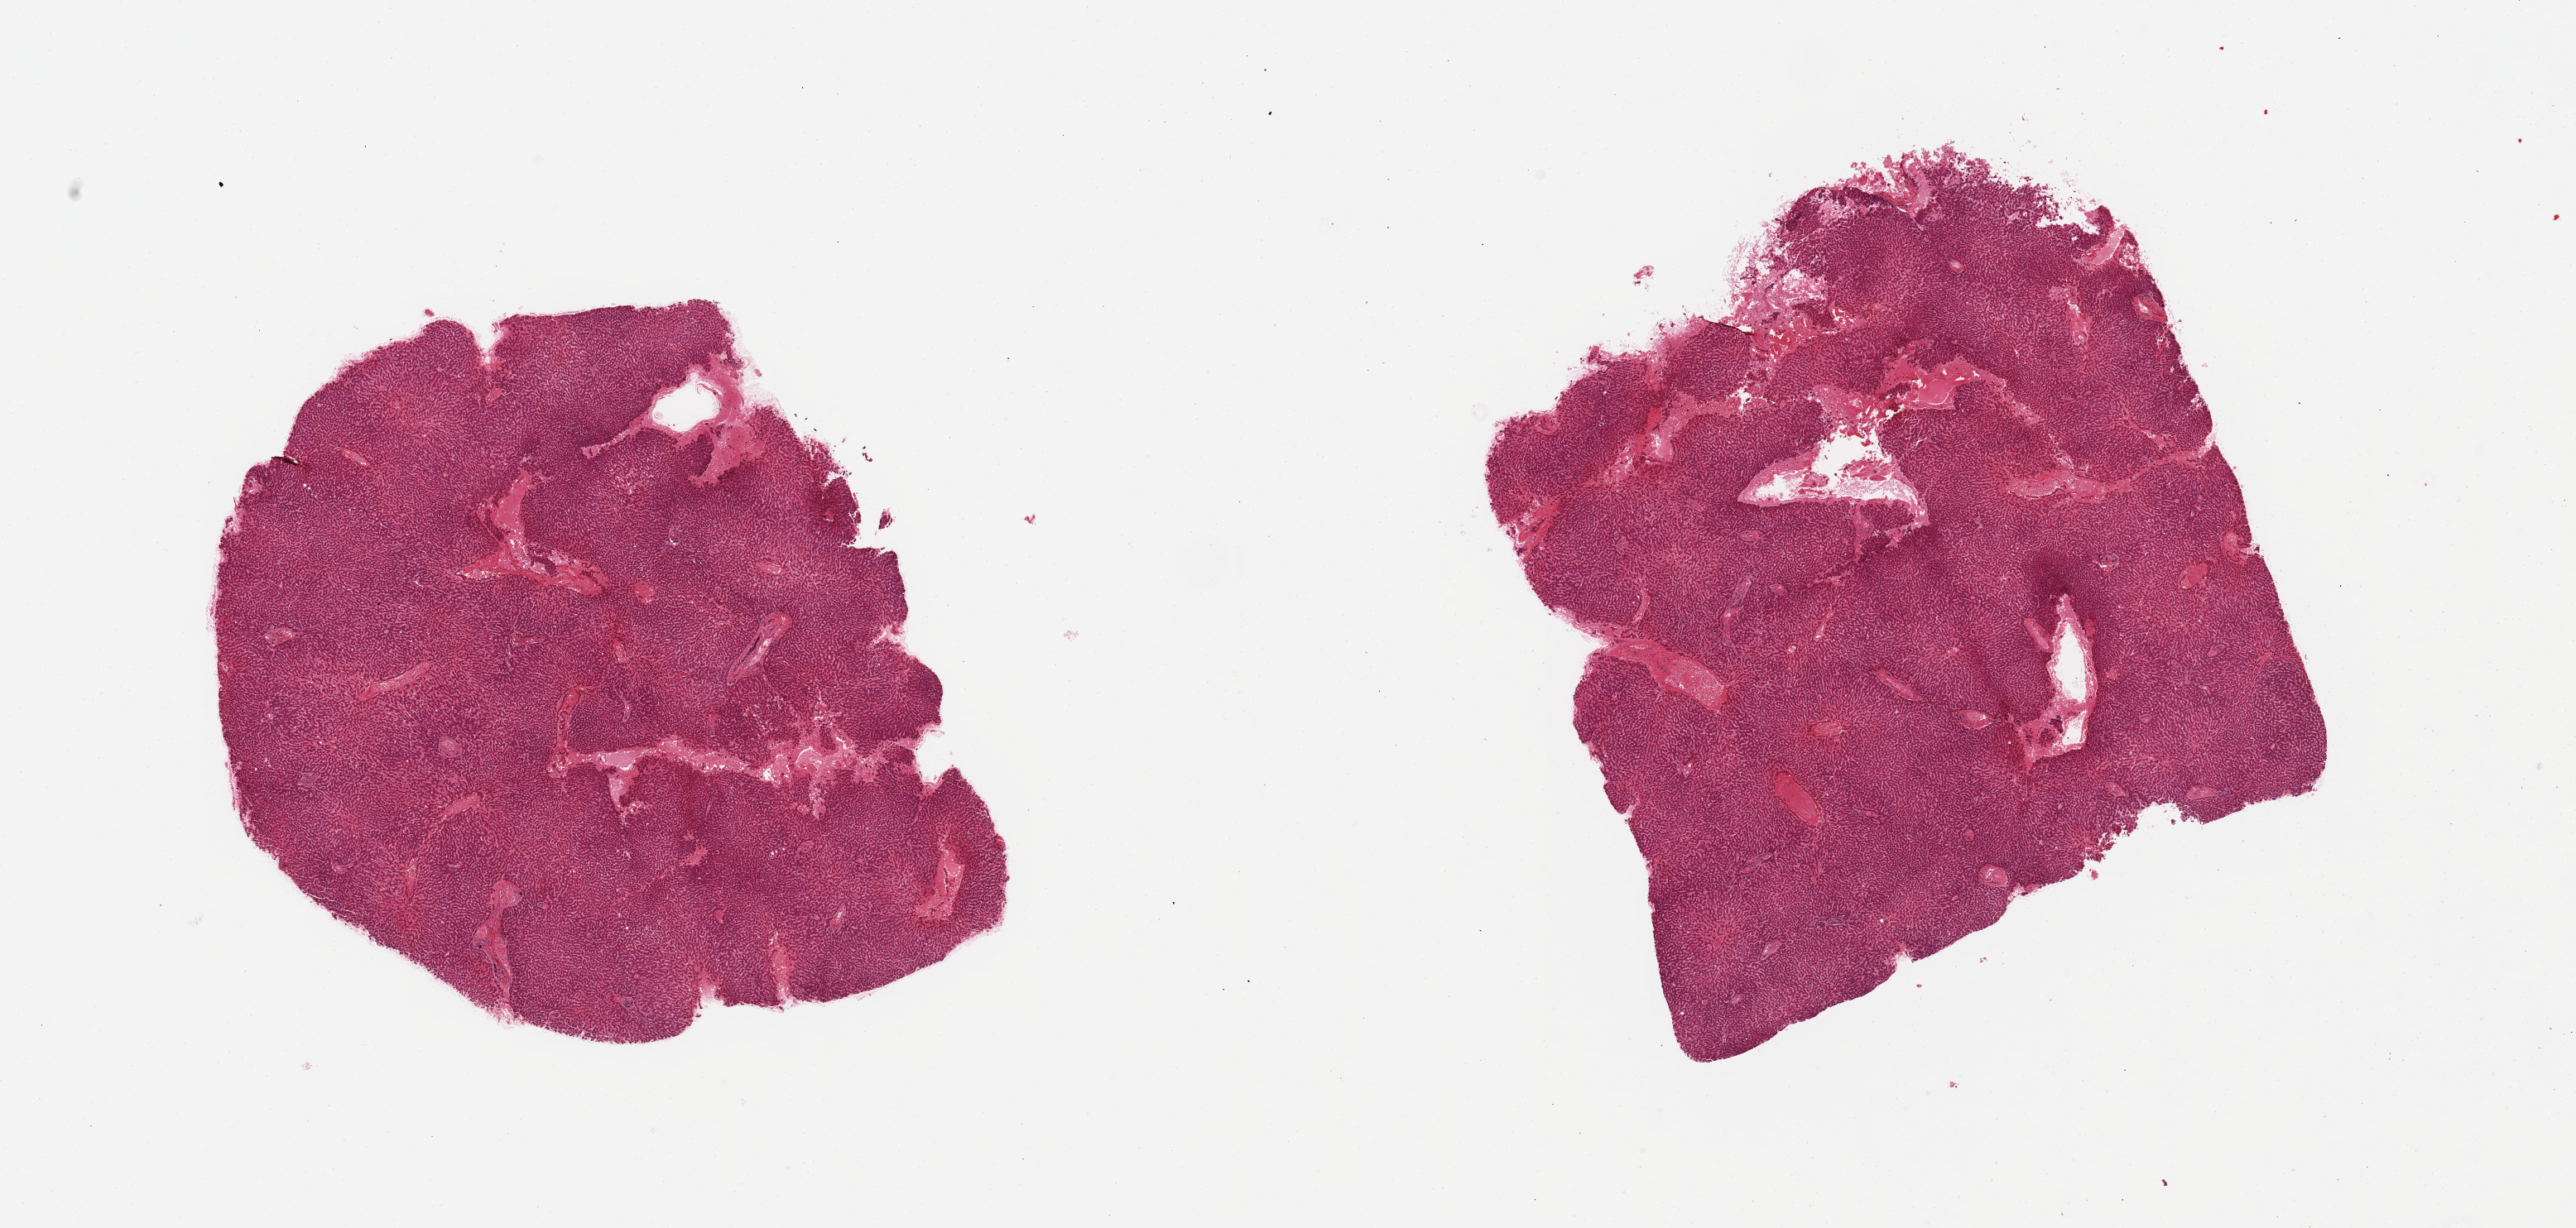
Hematoxylin and eosin (H&E) whole-slide image, brightfield, a low-resolution overview of the entire scanned area, about 24.6 x 11.7 mm. PAXgene-fixed paraffin-embedded (PFPE) section. Target tissue: liver. Tissue donor sample.
Reviewer comment on this tissue sample: 2 pieces; moderate vascular congestion.